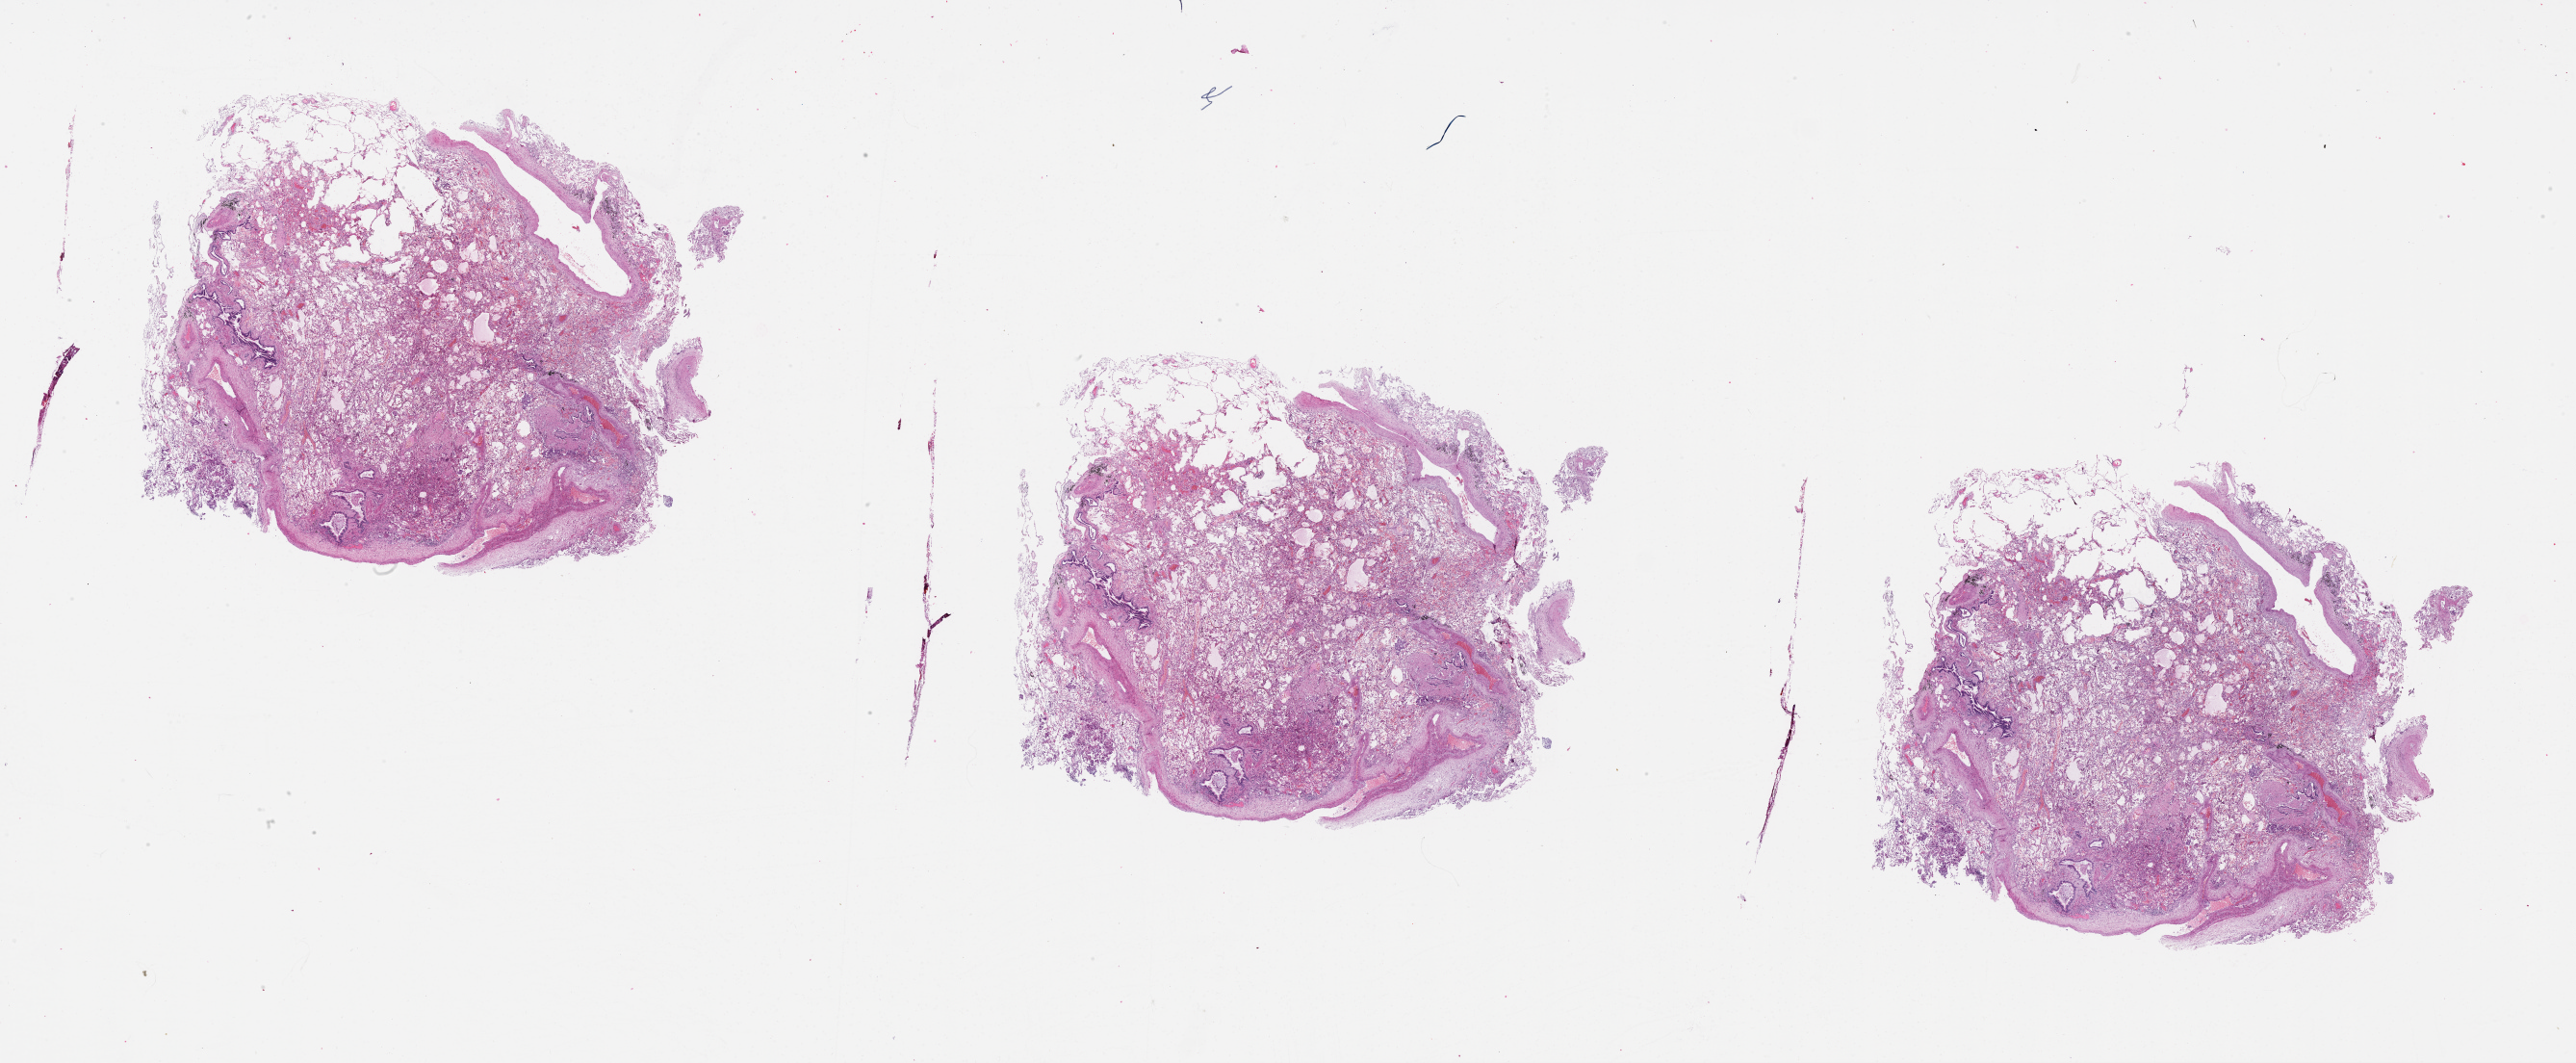
H&E whole-slide image — a low-resolution overview of the entire scanned area, about 43.1 x 17.8 mm (slide scanned at 20x), lung, tissue type not recorded.
Patient diagnosis (cohort enrolment): lung adenocarcinoma (lung).